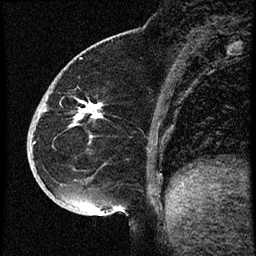
Breast MRI (dynamic contrast-enhanced), one sagittal slice; position 19 of 60 along the scan axis; dynamic contrast-enhanced study with each time point stored as its own series, time point 2 of 3 at this slice position (early post-contrast, ordered by acquisition time); 1.5 T; TE 4.2 ms, TR 18.9 ms; 2 mm slice thickness; 256 × 256 image matrix, field of view 200 × 200 mm. Female patient. From the clinical record (not read from this slice): setting: breast cancer imaged before/during neoadjuvant chemotherapy; receptor status: HR-positive, HER2-negative.
Structures marked on this image (semi-automatically segmented with operator editing):
- analysis volume of interest (the breast-tissue region the enhancement analysis was run in; not a lesion): box from (x=30, y=87) to (x=113, y=173) px
- tumour enhancement mask (voxels above the 100 % enhancement threshold inside the analysis volume of interest): (x=82, y=104)–(x=102, y=118)